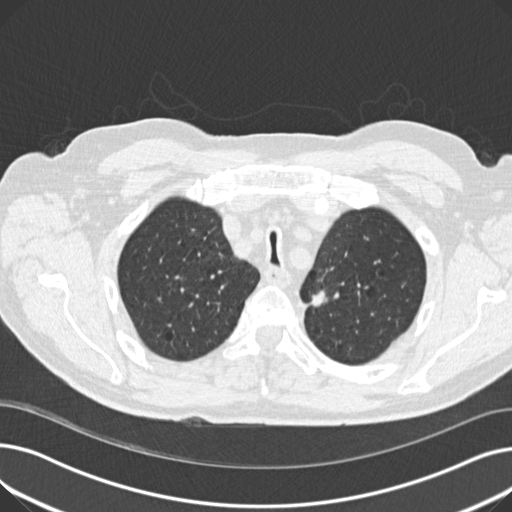
Low-dose screening chest CT, one axial slice; position 149 of 191 along the scan axis; reconstruction kernel B30f; lung window (W 1500 / L -600 HU); 2 mm slice thickness; 512 × 512 image matrix, field of view 370 × 370 mm.
Outlined on this slice (outlined manually by an expert reader):
- lesion 1 (tumor, upper lobe of left lung): bounding box (x1, y1, x2, y2) in pixels: (311, 291, 327, 306)